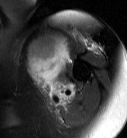
MRI of an extremity soft-tissue mass, one axial slice; position 57 of 87 along the scan axis; T2-weighted fat-saturated; MR volume resampled by the dataset authors to the PET/CT grid (not the native acquisition matrix); 3.27 mm slice thickness; 127 × 138 image matrix. Female patient. Case-level facts recorded for this patient, not image findings: histological type: pleiomorphic leiomyosarcoma; grade: high; site of the primary tumour: left biceps.
Annotated regions visible in this slice (expert contour drawn on MRI and transferred to this co-registered scan by the dataset authors):
- gross tumour volume including surrounding oedema: bounding box <27,34,69,95> (left, top, right, bottom; pixels)
- gross tumour volume (mass): <27,34,69,86>